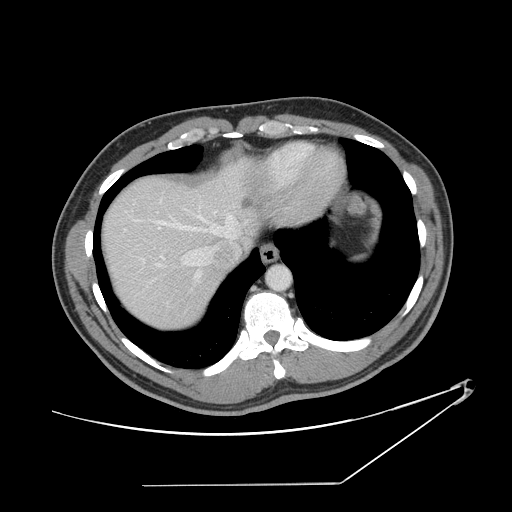
Contrast-enhanced abdominal CT, one axial slice. Slice 126 of 152 in the series (ordered by position). Reconstruction kernel STANDARD. 120 kVp. Intravenous contrast given. Soft-tissue window (W 400 / L 40 HU). 512 × 512 image matrix, field of view 432 × 432 mm. Male patient, age 45 years. Case-level facts recorded for this patient, not image findings: diagnosis: colorectal cancer liver metastases, imaged before liver resection; multiple liver metastases: no; largest metastasis: 1 cm; disease in both lobes: no.
Structures marked on this image (expert manual segmentation):
- hepatic veins: box from (x=124, y=198) to (x=238, y=281) px
- liver: (x=104, y=163)–(x=259, y=328)
- planned liver remnant (the part of the liver to remain after resection): (x=104, y=178)–(x=233, y=327)
- liver metastasis: (x=241, y=196)–(x=254, y=212)